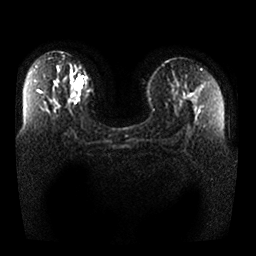
Breast MRI, one axial slice. Slice 17 of 25 in the series (ordered by position). Diffusion-weighted series; image 2 of 4 stored at this slice position (different b-values; order by instance number). 1.5 T. 256 × 256 image matrix, field of view 370 × 370 mm. Female patient.
Annotated regions visible in this slice (expert manual segmentation):
- tumour on diffusion-weighted imaging: bounding box (x1, y1, x2, y2) in pixels: (75, 77, 84, 91)